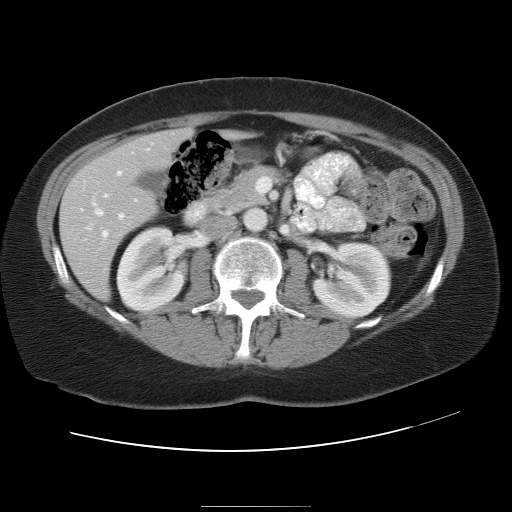
Contrast-enhanced abdominal CT, one axial slice; slice 14 of 30 in the series (ordered by position); 120 kVp; intravenous contrast given; soft-tissue window (W 400 / L 40 HU); 512 × 512 image matrix, field of view 376 × 376 mm. Female patient, age 52 years. Case-level facts recorded for this patient, not image findings: diagnosis: colorectal cancer liver metastases, imaged before liver resection; multiple liver metastases: no; largest metastasis: 3 cm.
Structures marked on this image (manually delineated by an expert):
- hepatic veins: bounding box [x1, y1, x2, y2] px = [95, 210, 102, 216]
- liver: [60, 128, 188, 298]
- planned liver remnant (the part of the liver to remain after resection): [163, 128, 188, 151]
- portal vein (with intrahepatic branches): [102, 172, 137, 236]